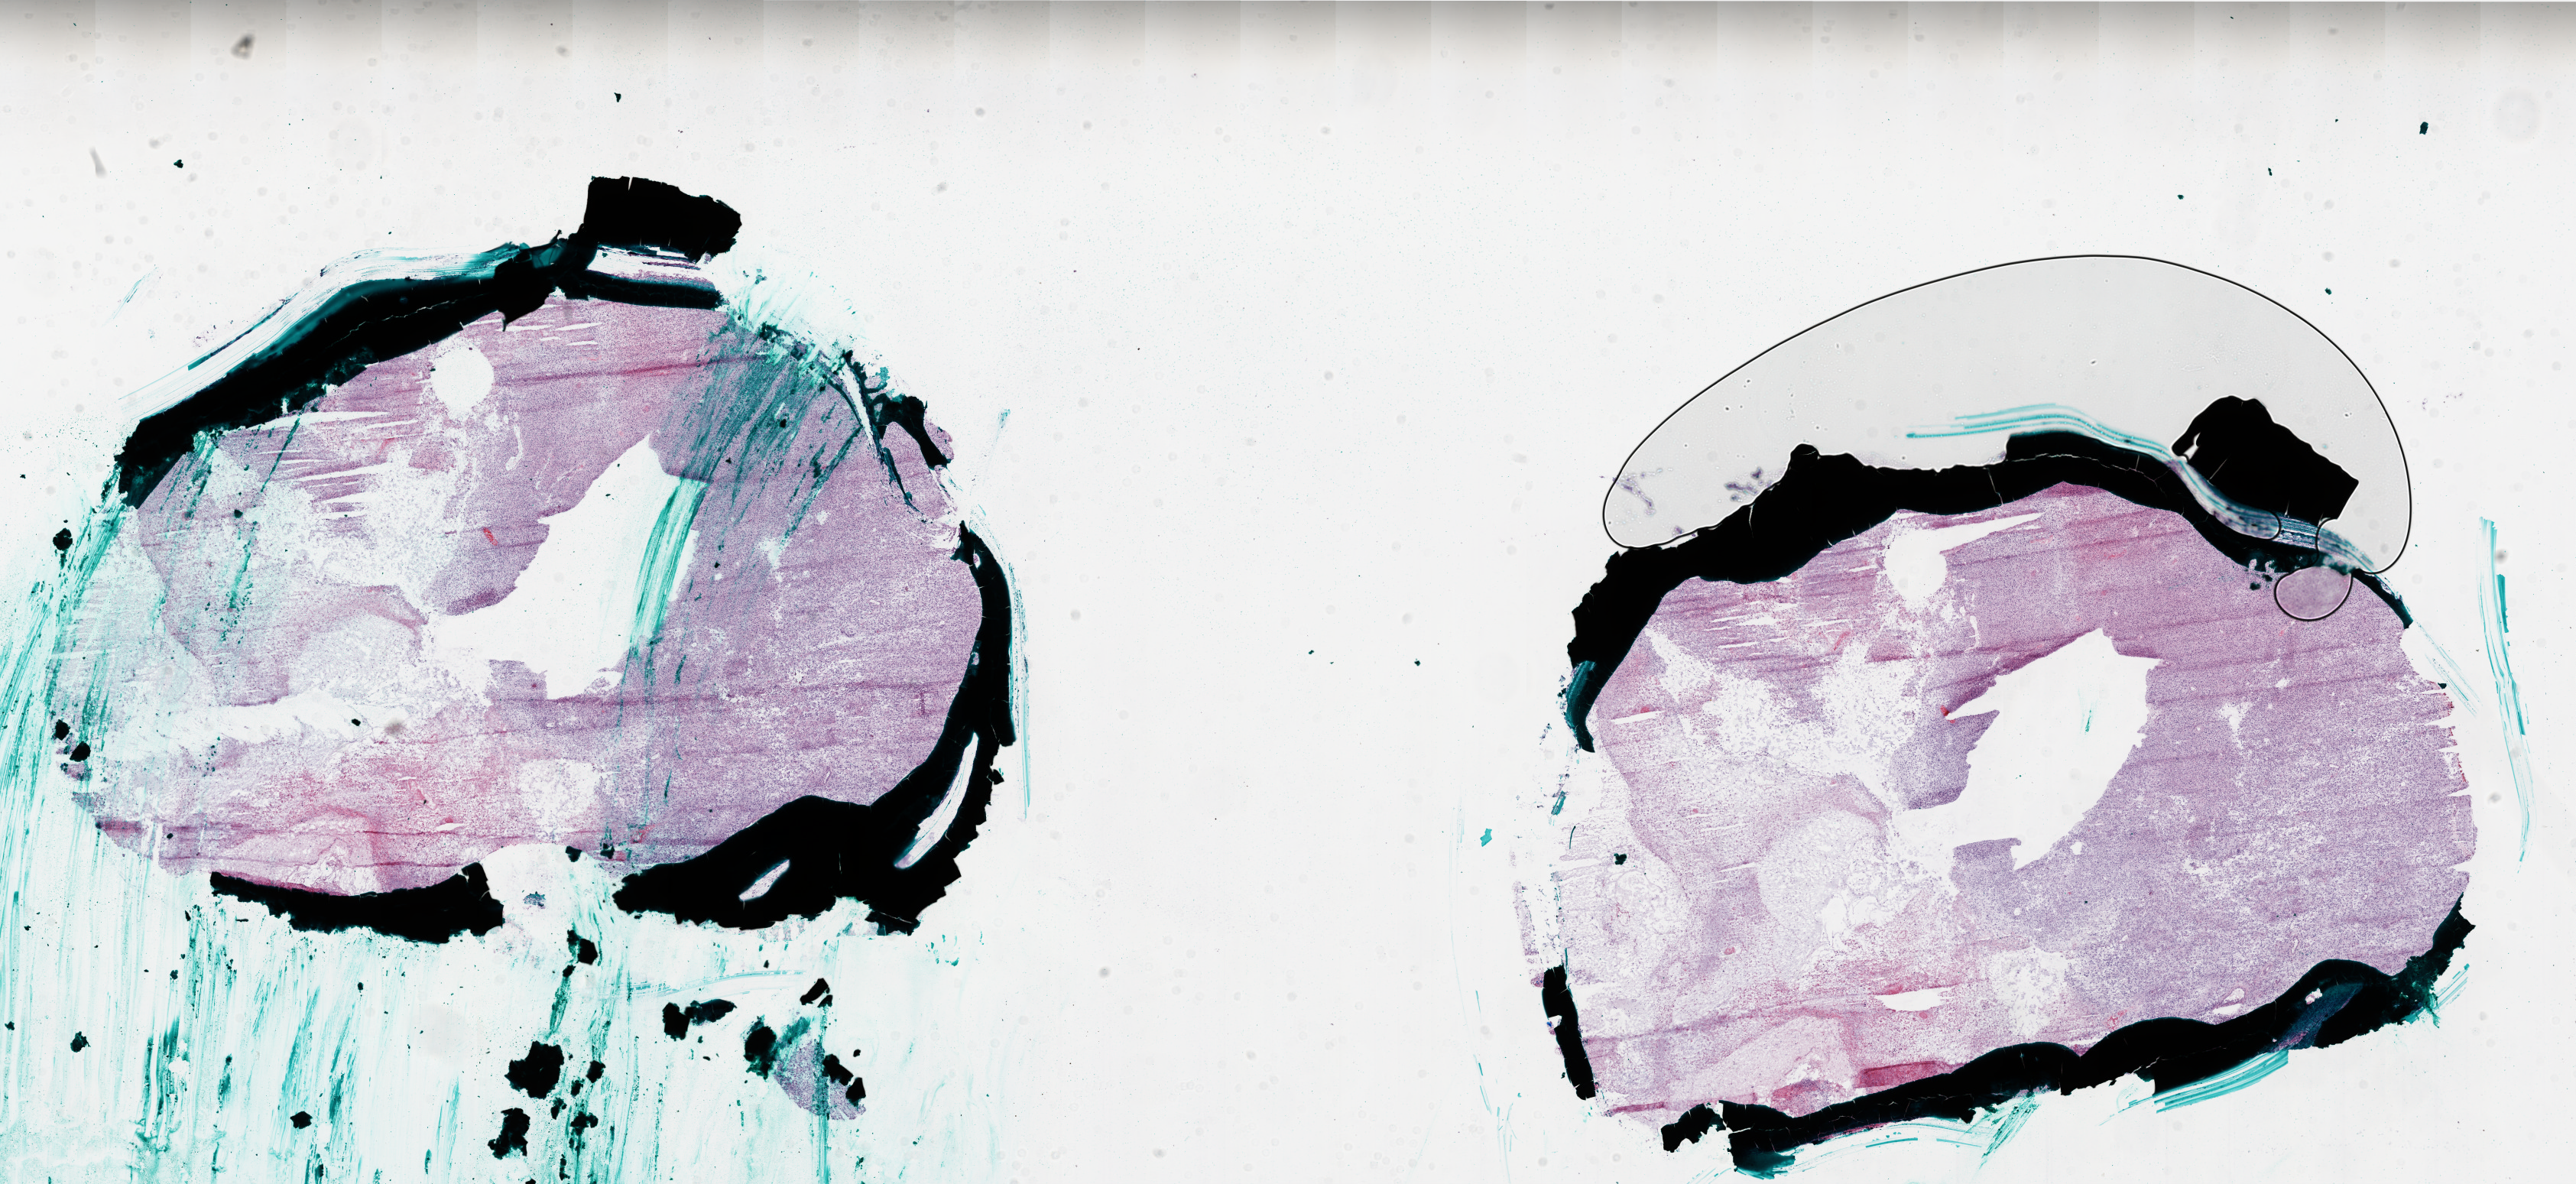
Whole-slide histology image, H&E-stained, low-resolution overview of the scanned area, about 27.0 x 12.4 mm (acquisition: 20x scan); frozen section from the top of the tissue portion; brain, primary tumour sample. Male, age 57 years at initial diagnosis. Composition of this section per pathologist review: tumour cells 60%, tumour nuclei 100%, normal cells 0%, stromal cells 0%, necrosis 40%.
Diagnosis: Glioblastoma.